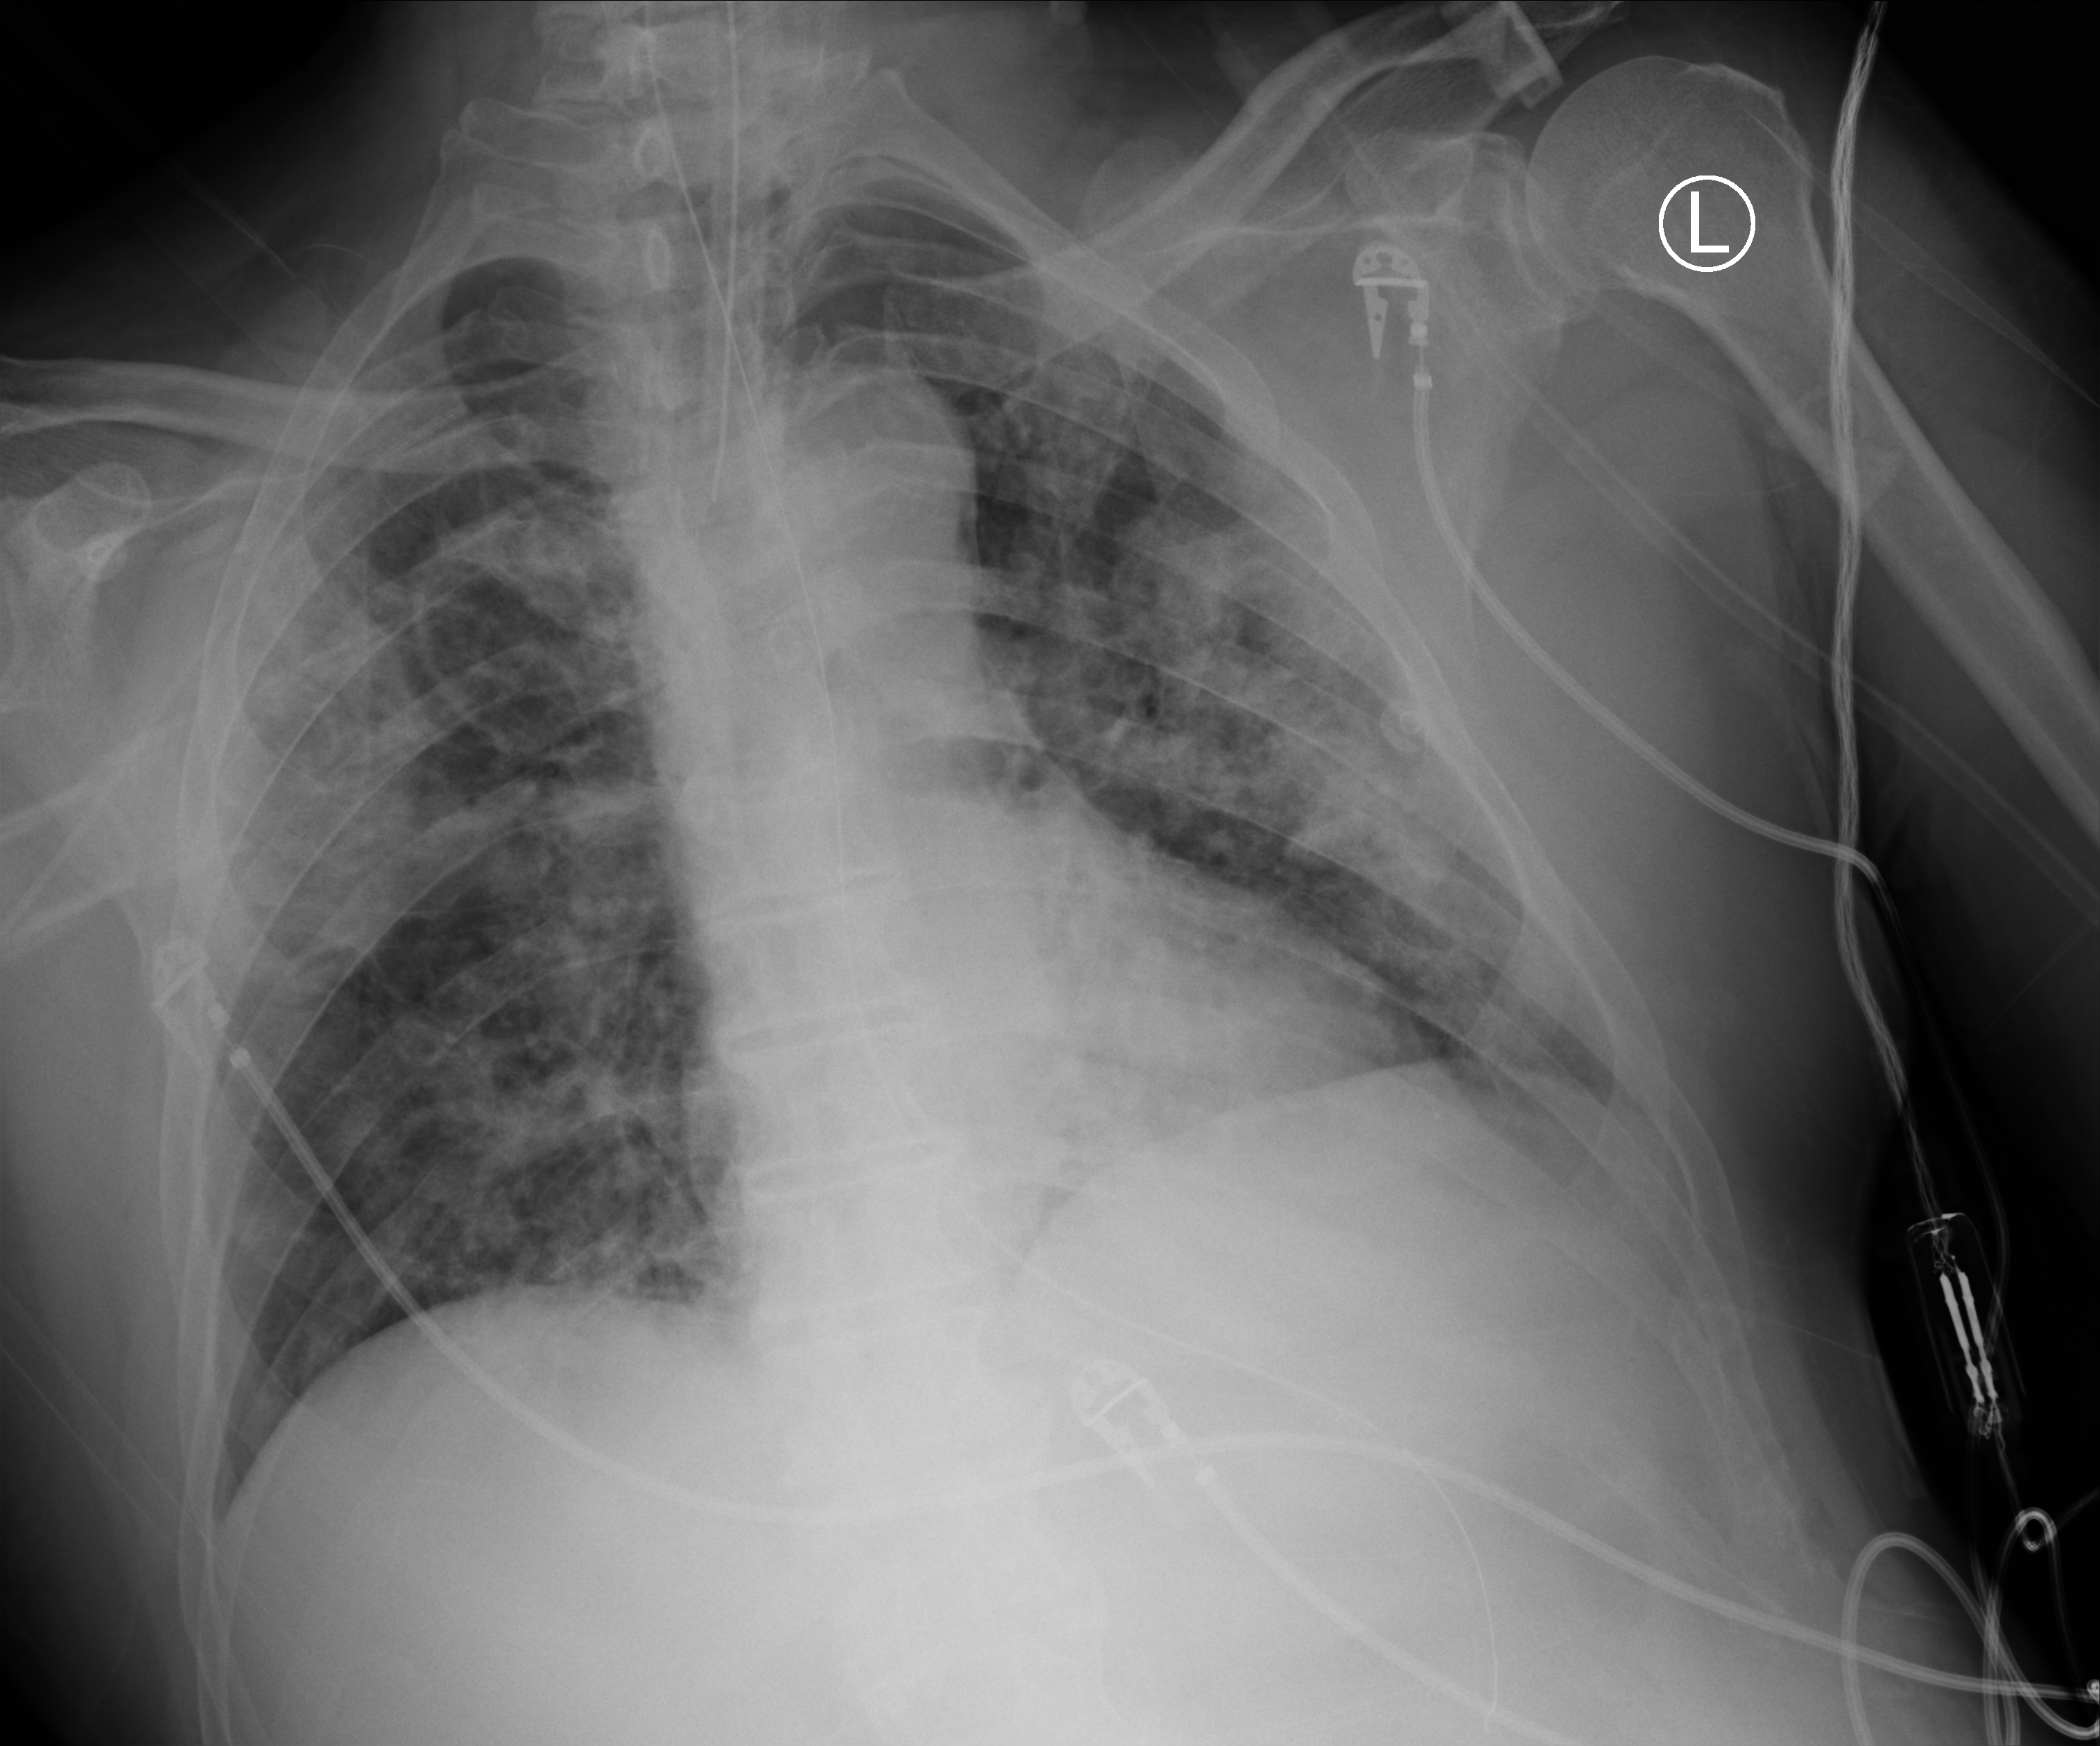
Chest X-ray (portable); anteroposterior (AP) projection. Patient hospitalised with COVID-19; male, aged 60–74 years.
From the hospital-stay record, not from the radiograph (when in the stay this image was taken is not recorded):
- chronic kidney disease (admission record): no